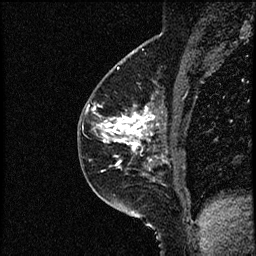
Breast MRI (dynamic contrast-enhanced), one sagittal slice; slice 34 of 52 in the series (ordered by position); dynamic contrast-enhanced study with each time point stored as its own series, time point 2 of 3 at this slice position (early post-contrast, ordered by acquisition time); 1.5 T; TE 4.2 ms, TR 17.6 ms; 2 mm slice thickness; 256 × 256 image matrix. Patient: female, 49 years. From the clinical record (not read from this slice): setting: breast cancer imaged before/during neoadjuvant chemotherapy; receptor status: HER2-positive.
Annotated regions visible in this slice (semi-automatic segmentation, software-assisted and operator-edited):
- analysis volume of interest (the breast-tissue region the enhancement analysis was run in; not a lesion): bounding box [x1, y1, x2, y2] px = [85, 65, 182, 175]
- tumour enhancement mask (voxels above the 100 % enhancement threshold inside the analysis volume of interest): [93, 105, 159, 168]